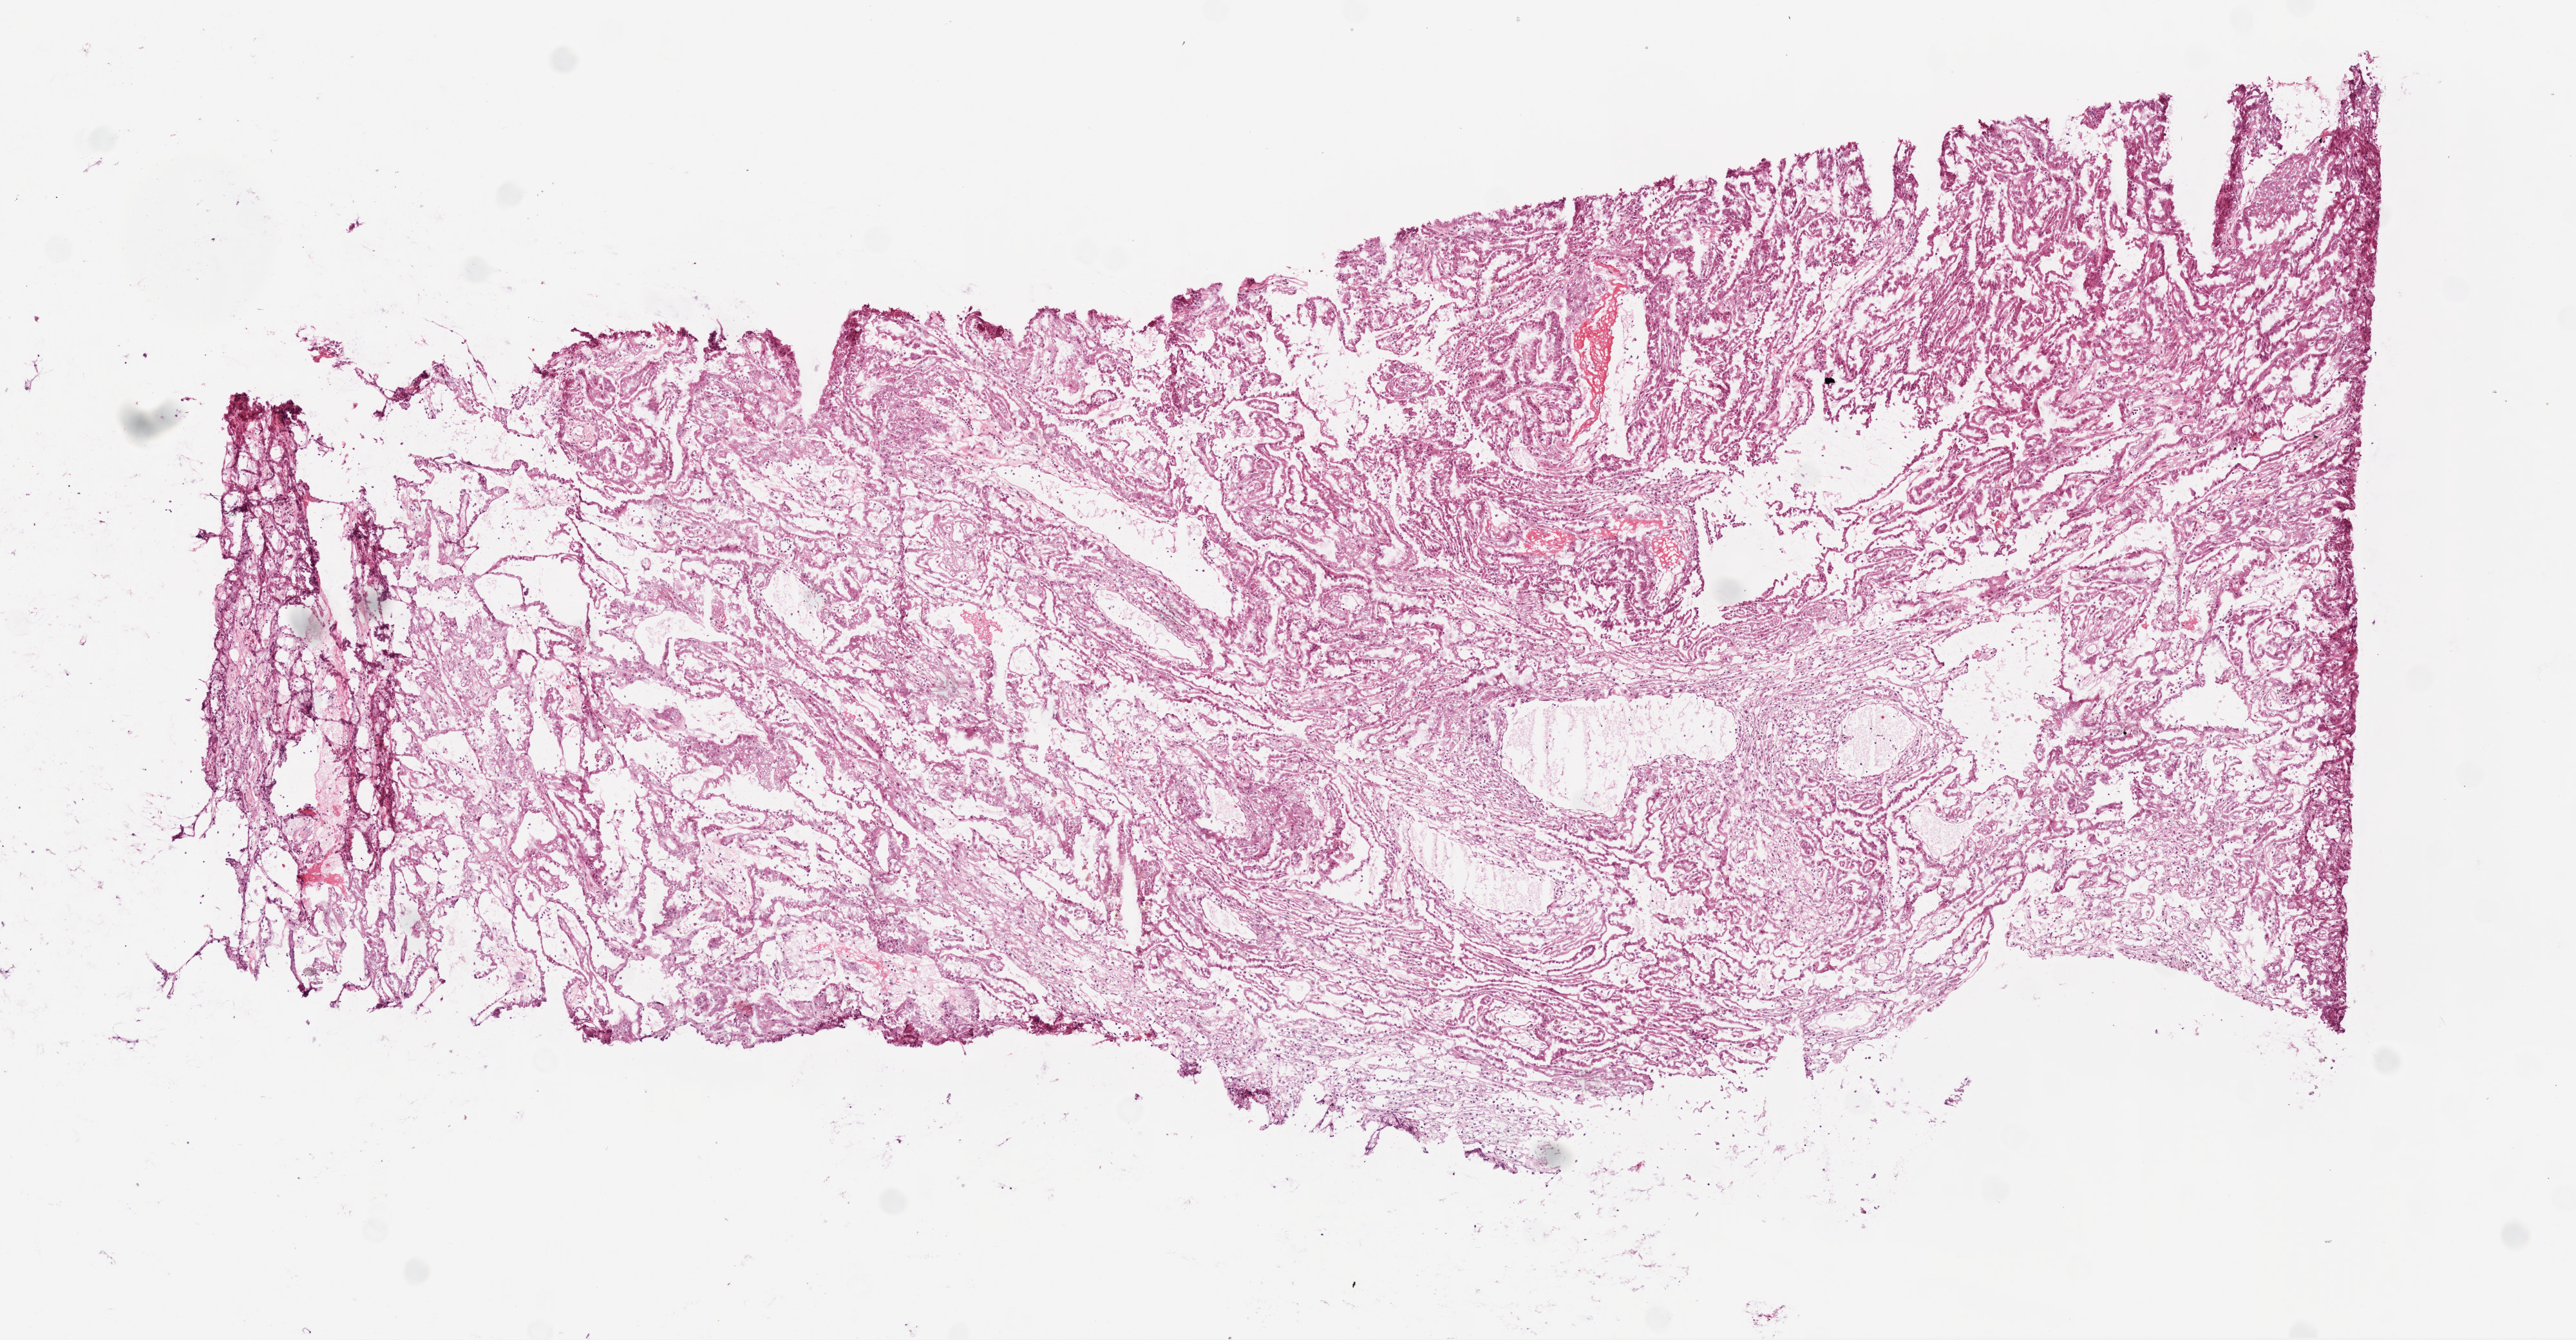
Whole-slide histology image, Hematoxylin and eosin (H&E) stained, shown as a low-resolution overview of the whole scanned area (about 8.0 x 4.2 mm, acquisition: 20x scan), frozen section from the top of the tissue portion, sample: primary tumour, kidney. Patient: male, age at initial diagnosis 63 years. Histologic grade: G3 (poorly differentiated). Slide review estimates, as recorded: tumour cells 90%, tumour nuclei 80%, normal cells 0%, stromal cells 10%, necrosis 0%.
TNM: T1b N0 M0. Diagnosis: Clear cell adenocarcinoma, NOS. AJCC pathologic stage: I (7th edition).